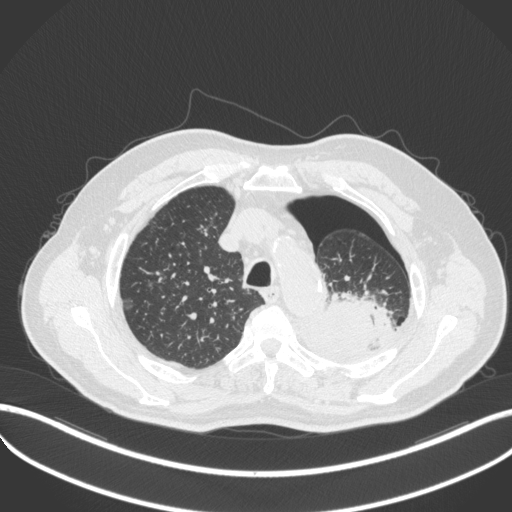
Chest CT, one axial slice. Slice 397 of 466 in the series (ordered by position). Reconstruction kernel B31f. 120 kVp. Lung window (W 1500 / L -600 HU). 1 mm slice thickness. 512 × 512 image matrix, field of view 400 × 400 mm. Patient: male, 76 years. From the clinical record (not read from this slice): clinical TNM (as recorded): T3 N0 M1b.
Annotated regions visible in this slice (bounding box drawn by a radiologist):
- lung tumour (recorded histology: adenocarcinoma): bounding box [x1, y1, x2, y2] px = [319, 282, 400, 357]